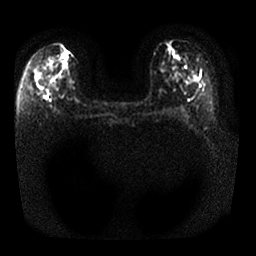
Breast MRI, one axial slice. Position 13 of 25 along the scan axis. Diffusion-weighted series; image 2 of 4 stored at this slice position (different b-values; order by instance number). 1.5 T. 4 mm slice thickness. 256 × 256 image matrix. Female patient.
Outlined on this slice (manually delineated by an expert):
- tumour on diffusion-weighted imaging: box from (x=40, y=68) to (x=50, y=88) px